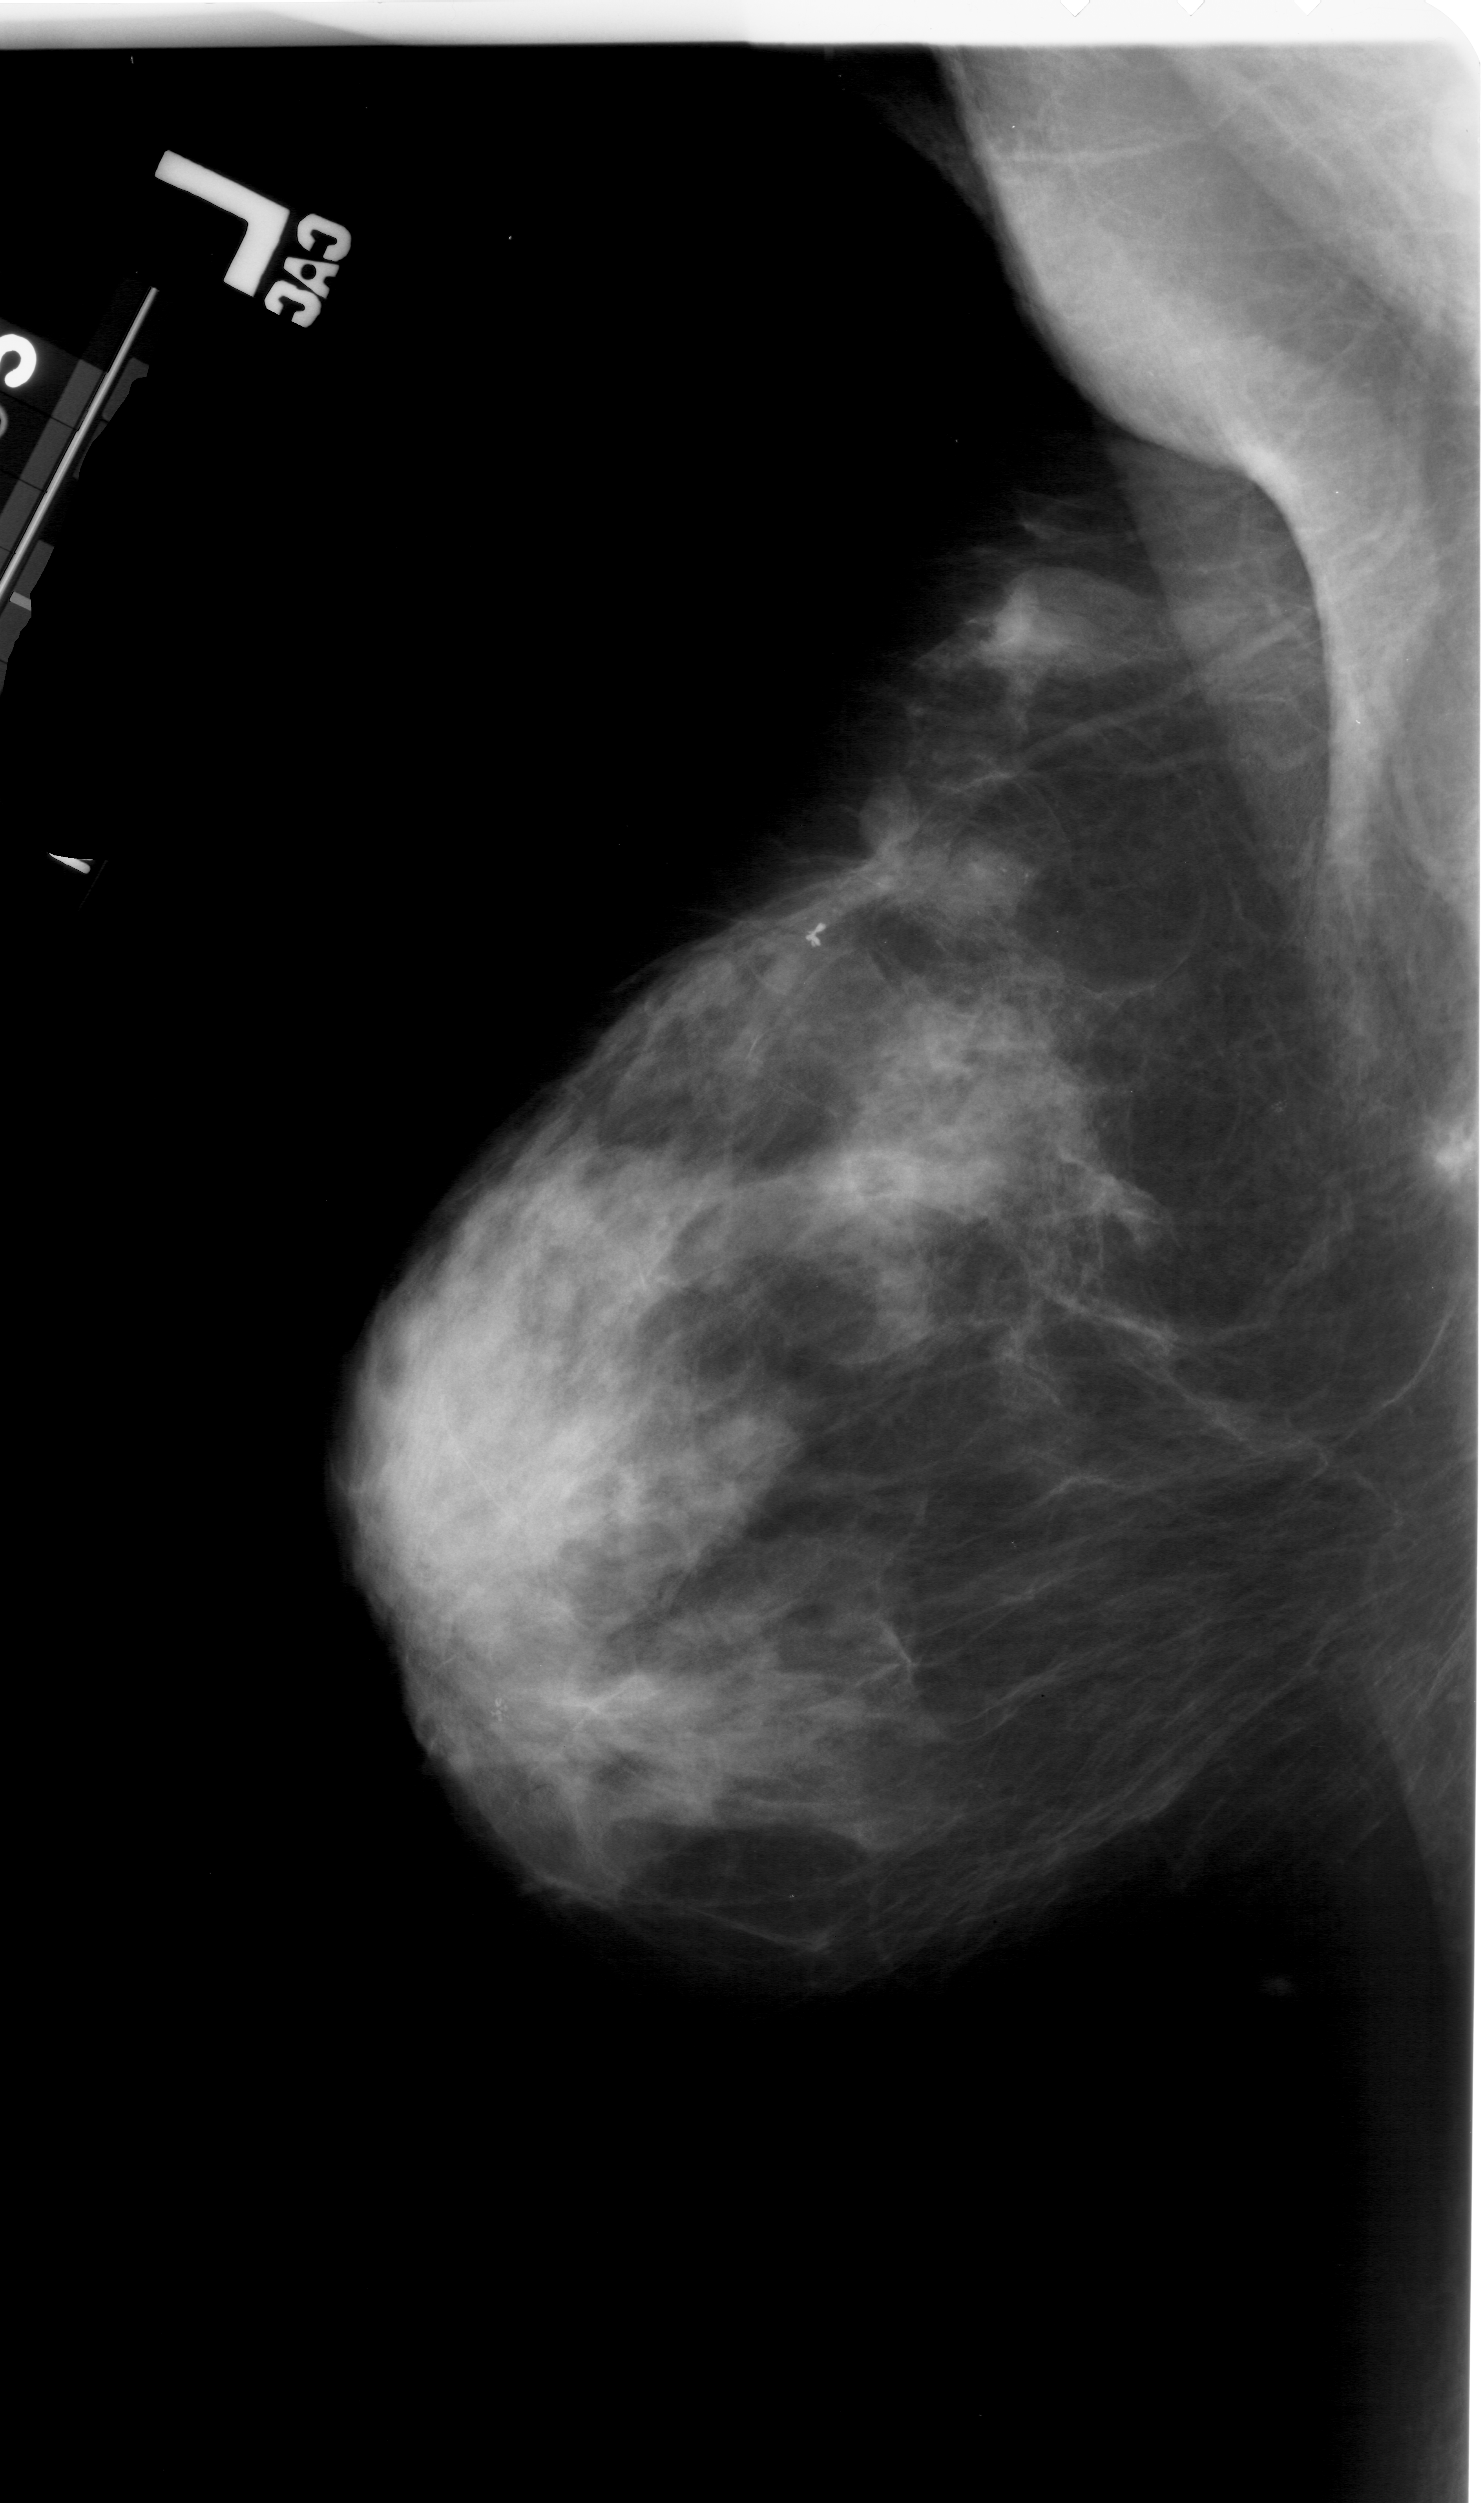
Digitized screen-film mammogram; left breast; MLO view; breast composition: extremely dense (BI-RADS density category 4 of 4); 1484 × 2503 image matrix.
Marked abnormalities (boxes around the expert regions of interest):
- mass, shape irregular, margins spiculated; BI-RADS assessment category 5; subtlety rating 4 on a 1 (subtle) to 5 (obvious) scale; pathology result (as recorded, not read from the image): malignant: box from (x=767, y=768) to (x=1057, y=959) px